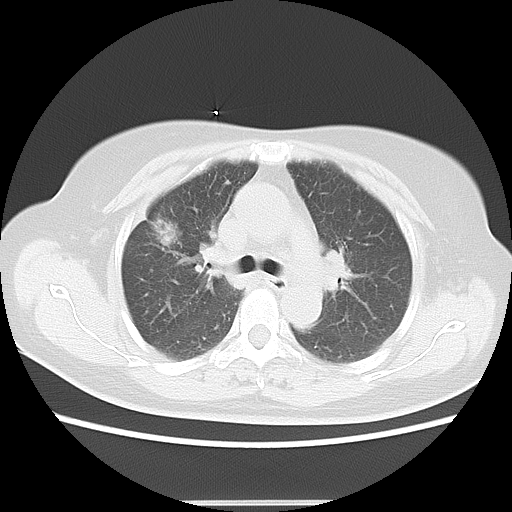
Chest CT, one axial slice. Slice 10 of 17 in the series (ordered by position). 120 kVp. Lung window (W 1500 / L -600 HU). 5 mm slice thickness. 512 × 512 image matrix, field of view 350 × 350 mm. Female patient, age 57 years. From the clinical record (not read from this slice): clinical TNM (as recorded): T1c N1 M0.
Outlined on this slice (rectangle marked by the reading radiologist):
- lung tumour (recorded histology: adenocarcinoma): bounding box [x1, y1, x2, y2] px = [148, 212, 186, 255]